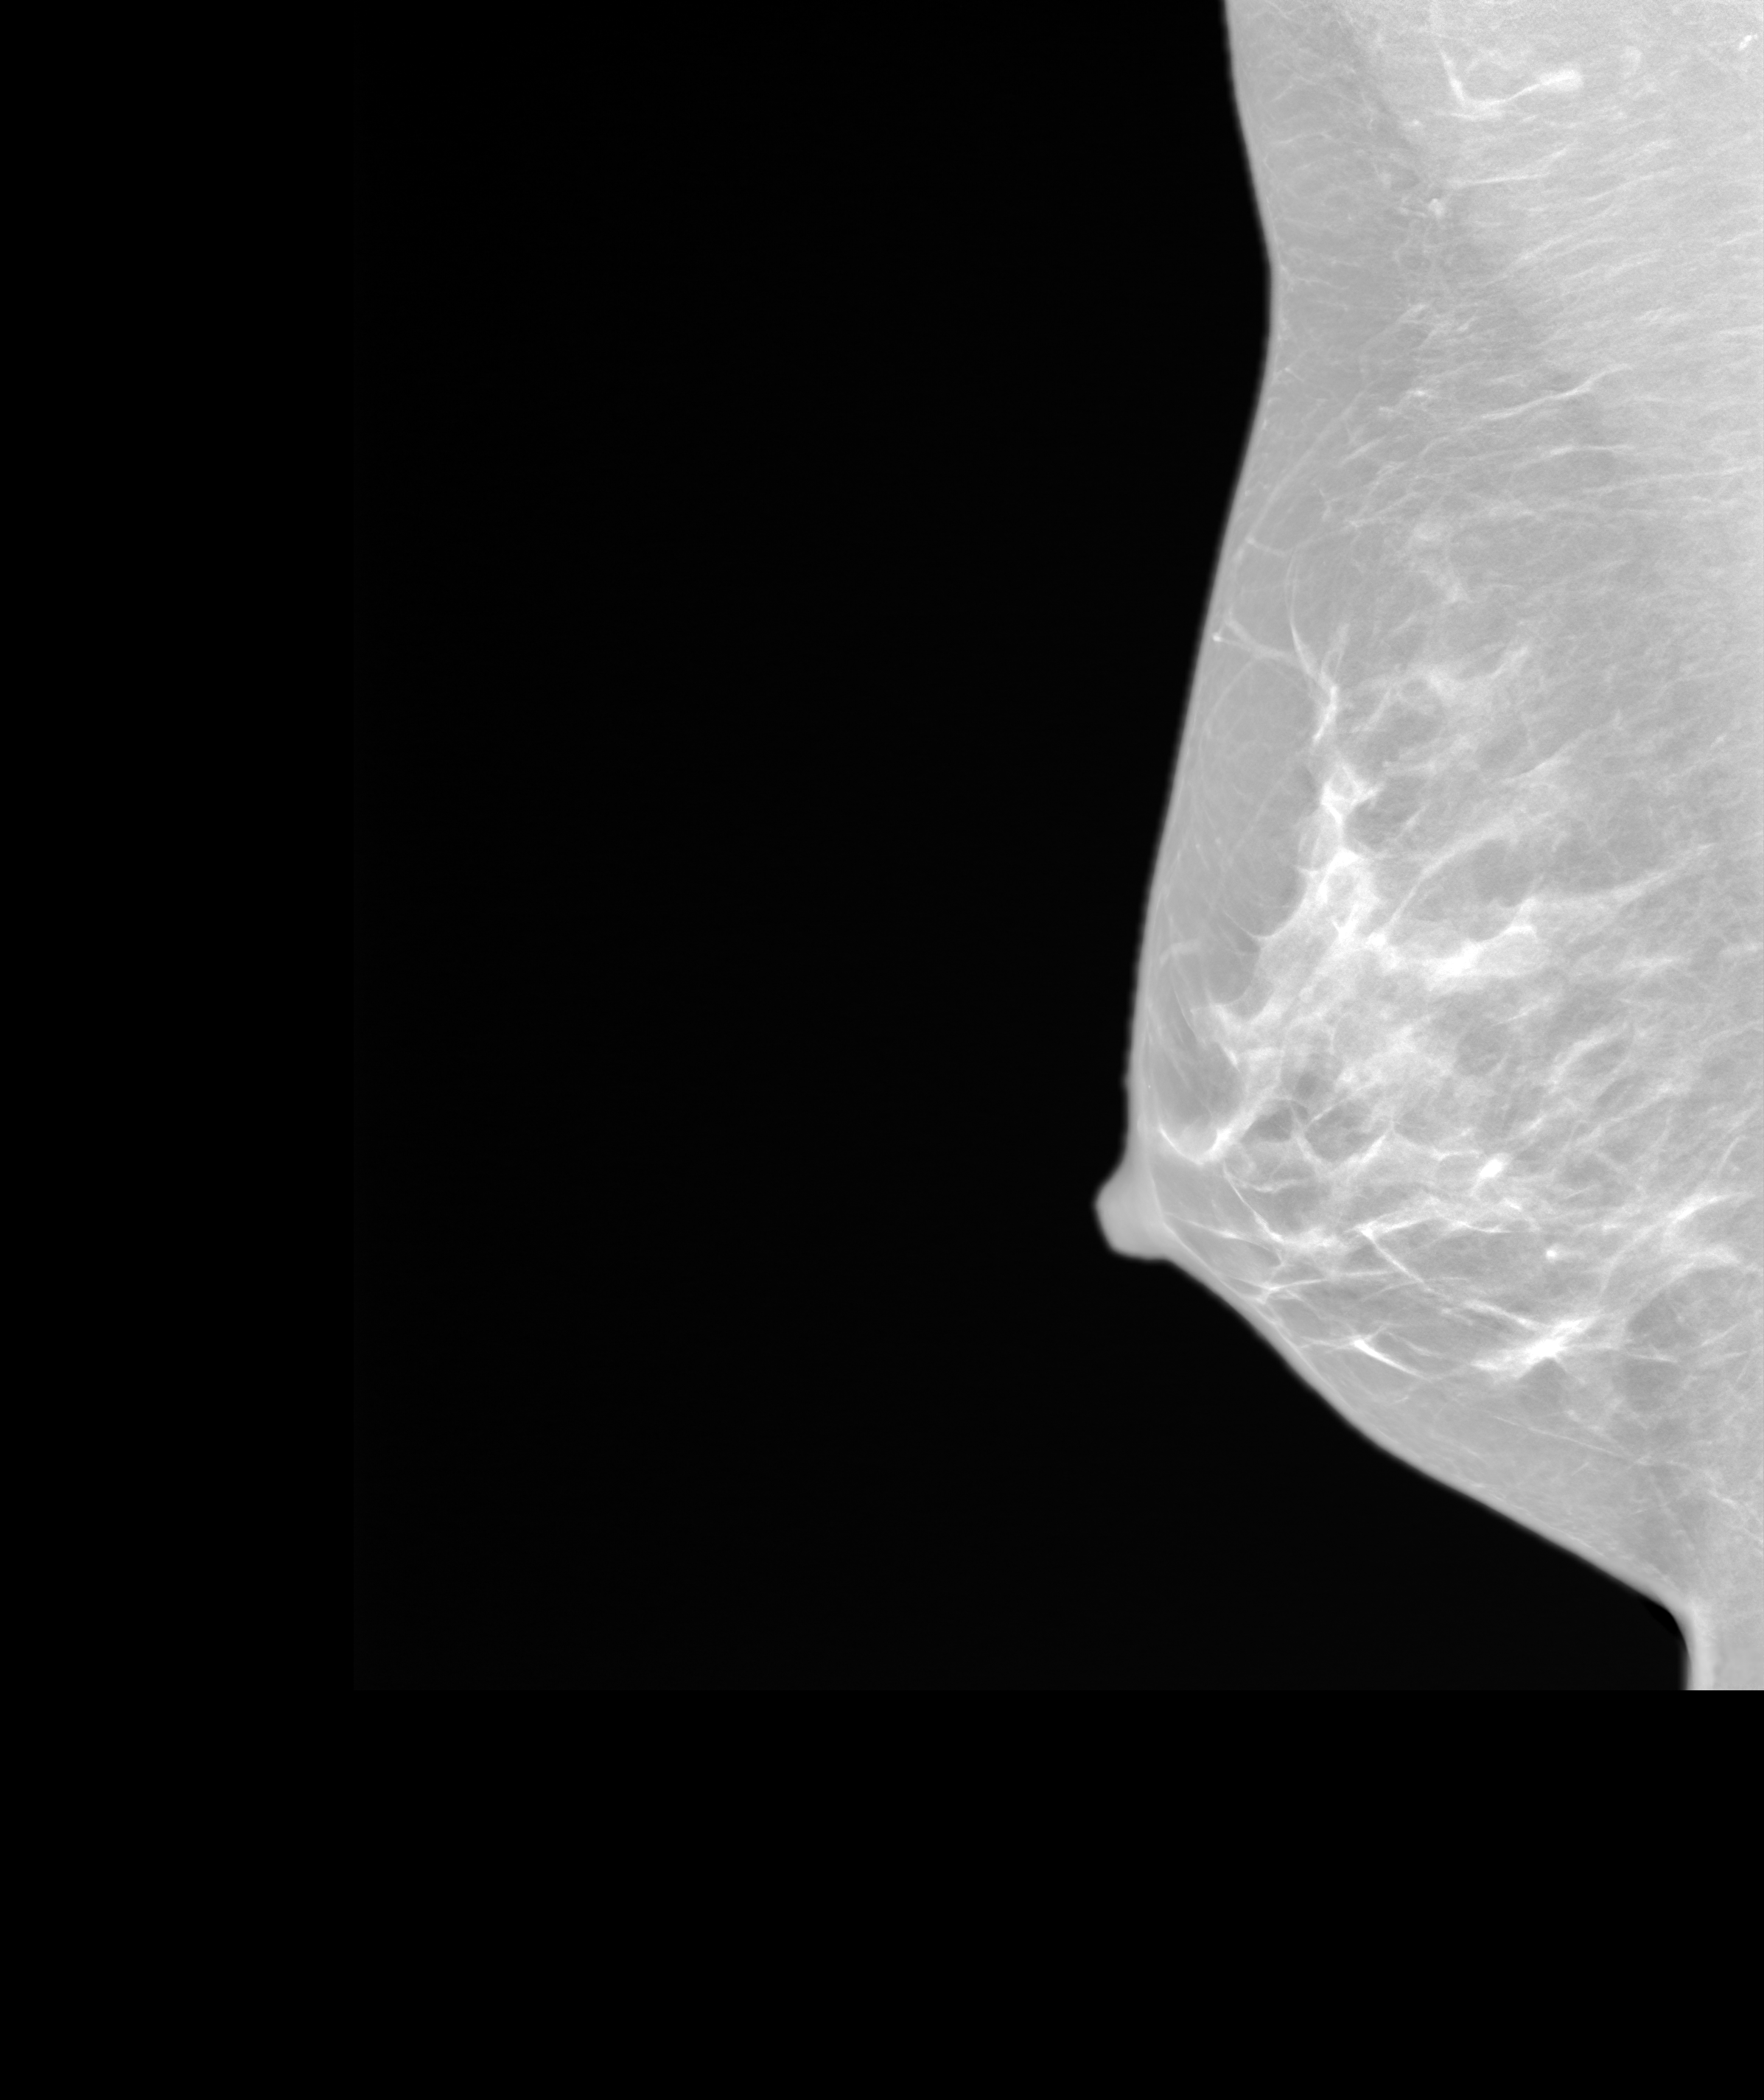
Screening examination. Patient: female, 44 years.
Image type: synthesized 2-D view from tomosynthesis. Breast: right. Projection: medio-lateral oblique projection.